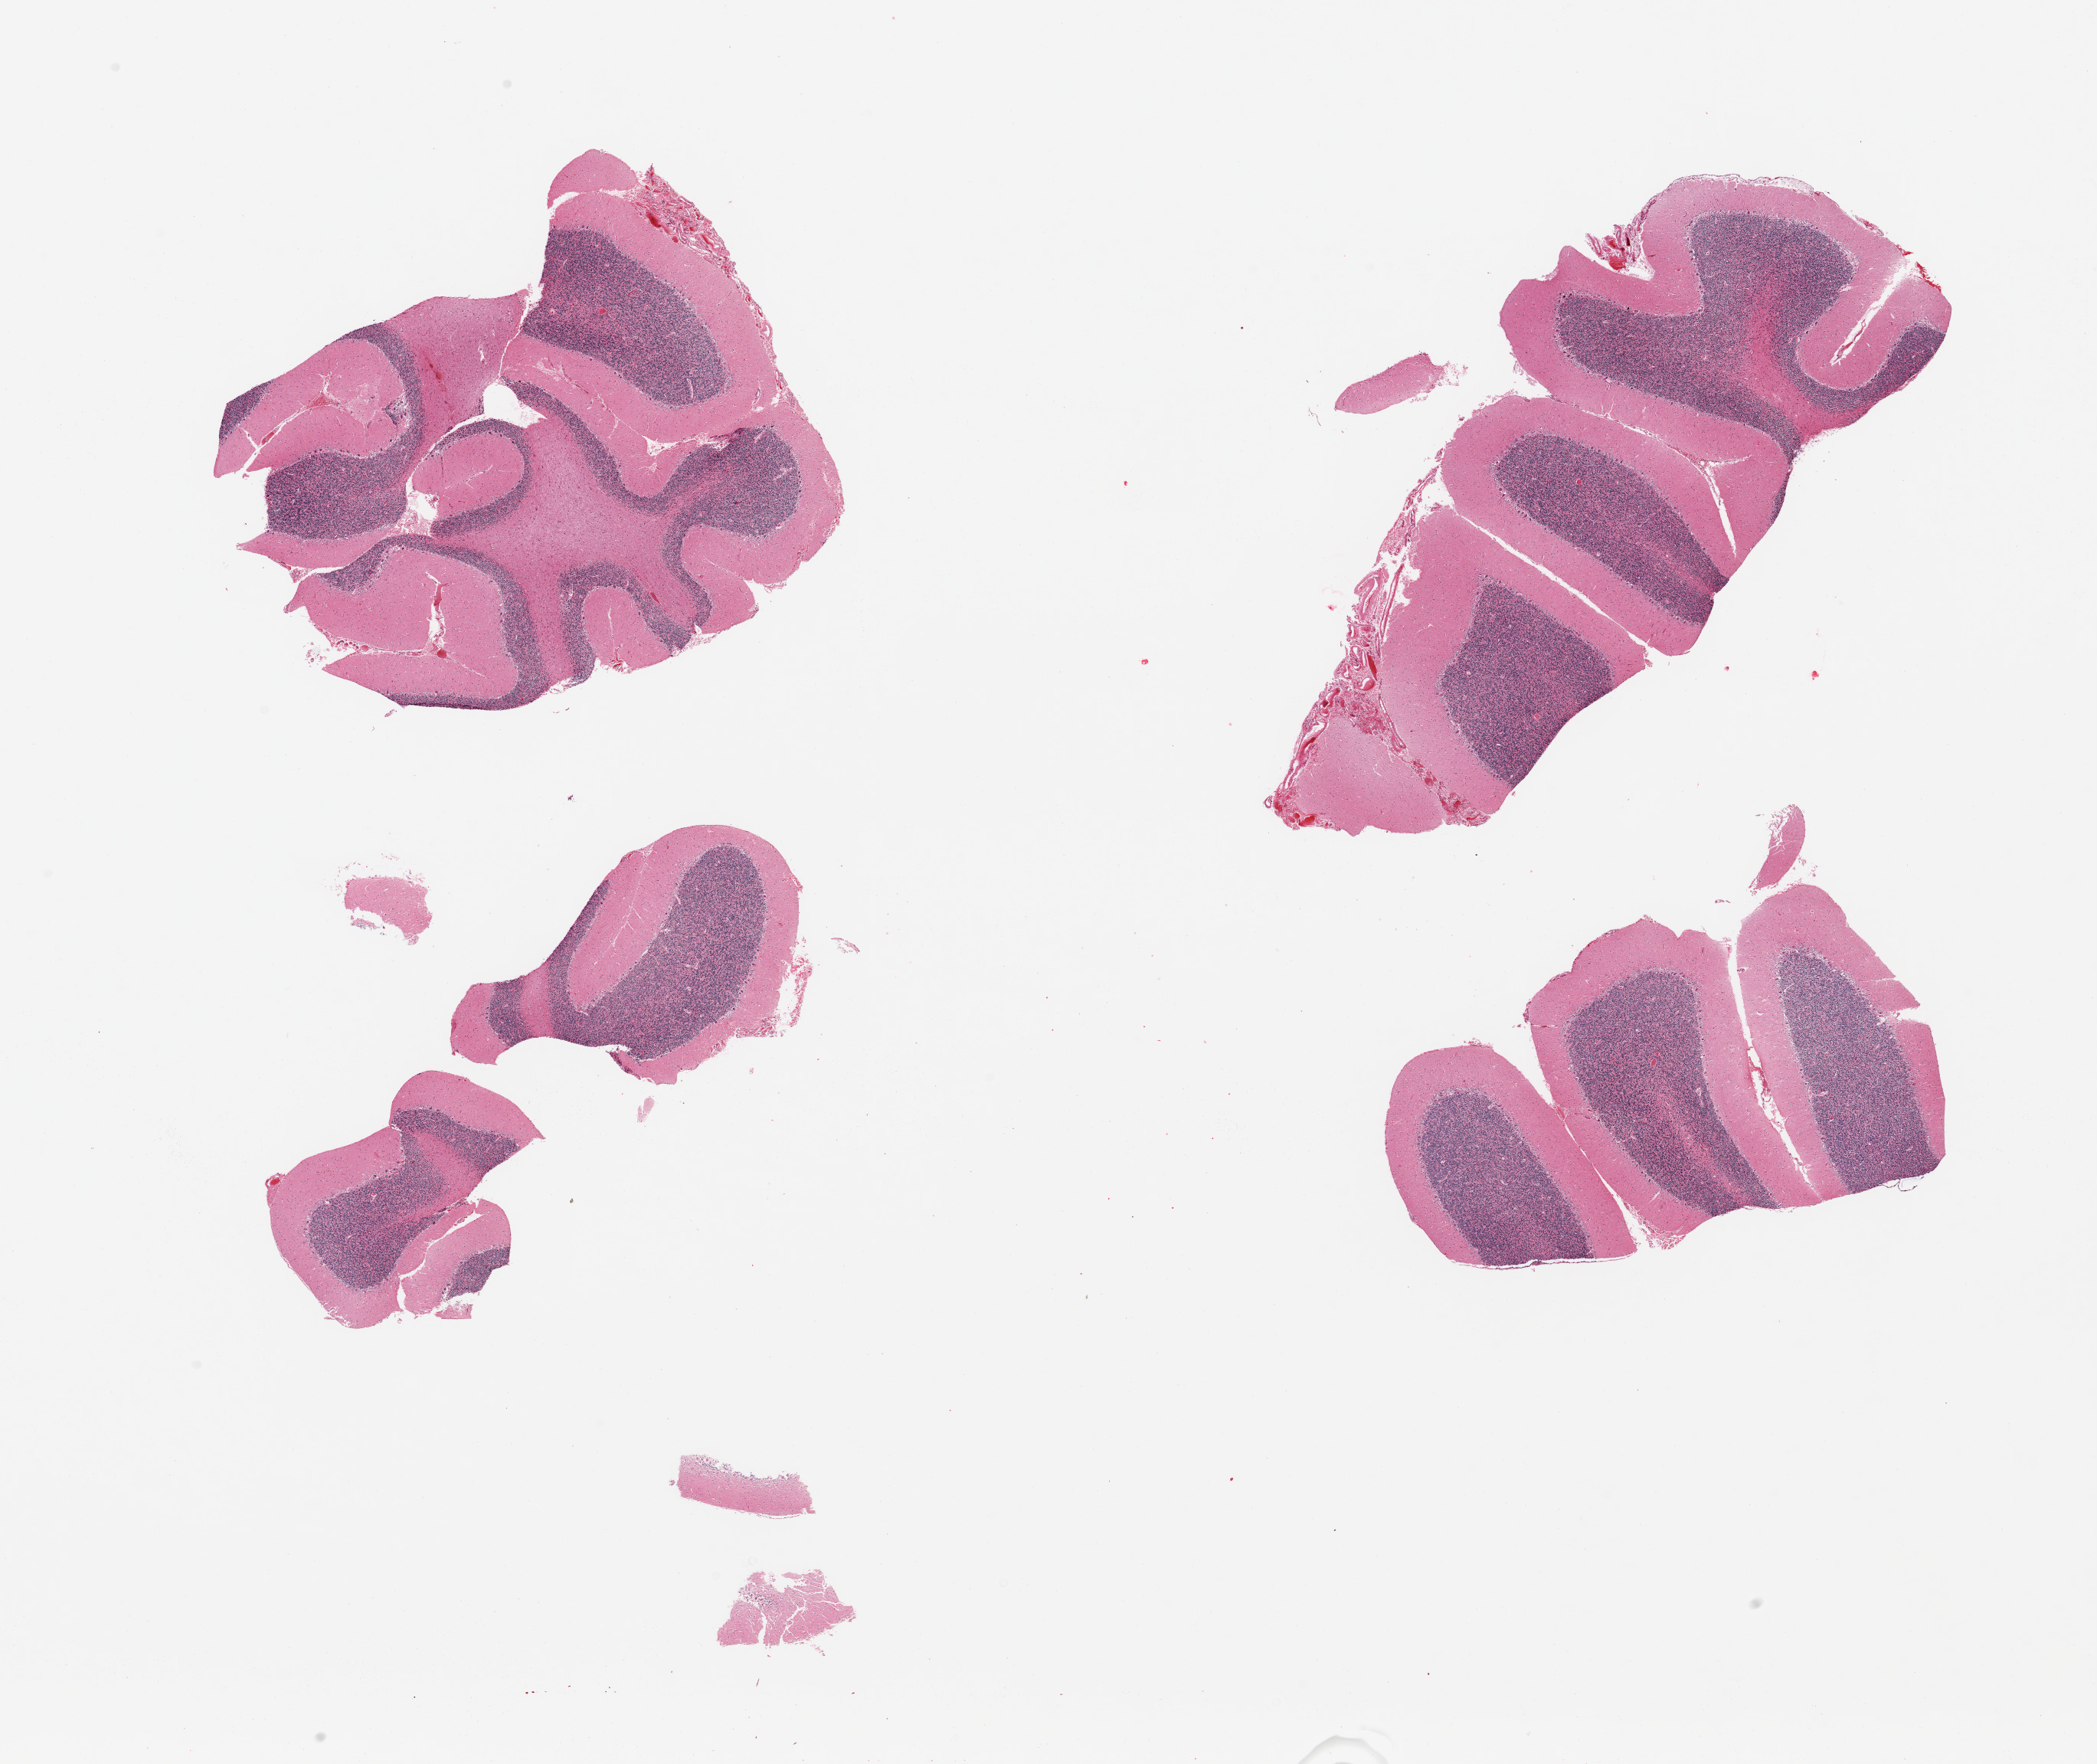
Digitized haematoxylin and eosin-stained section, a low-resolution overview of the entire scanned area, about 21.7 x 18.2 mm (slide scanned at 20x); PAXgene-fixed paraffin-embedded (PFPE) section; section of cerebellum (target tissue); tissue donor sample. Donor sex: male.
* reviewer comment on this tissue sample: 4 pieces, no abnormalities